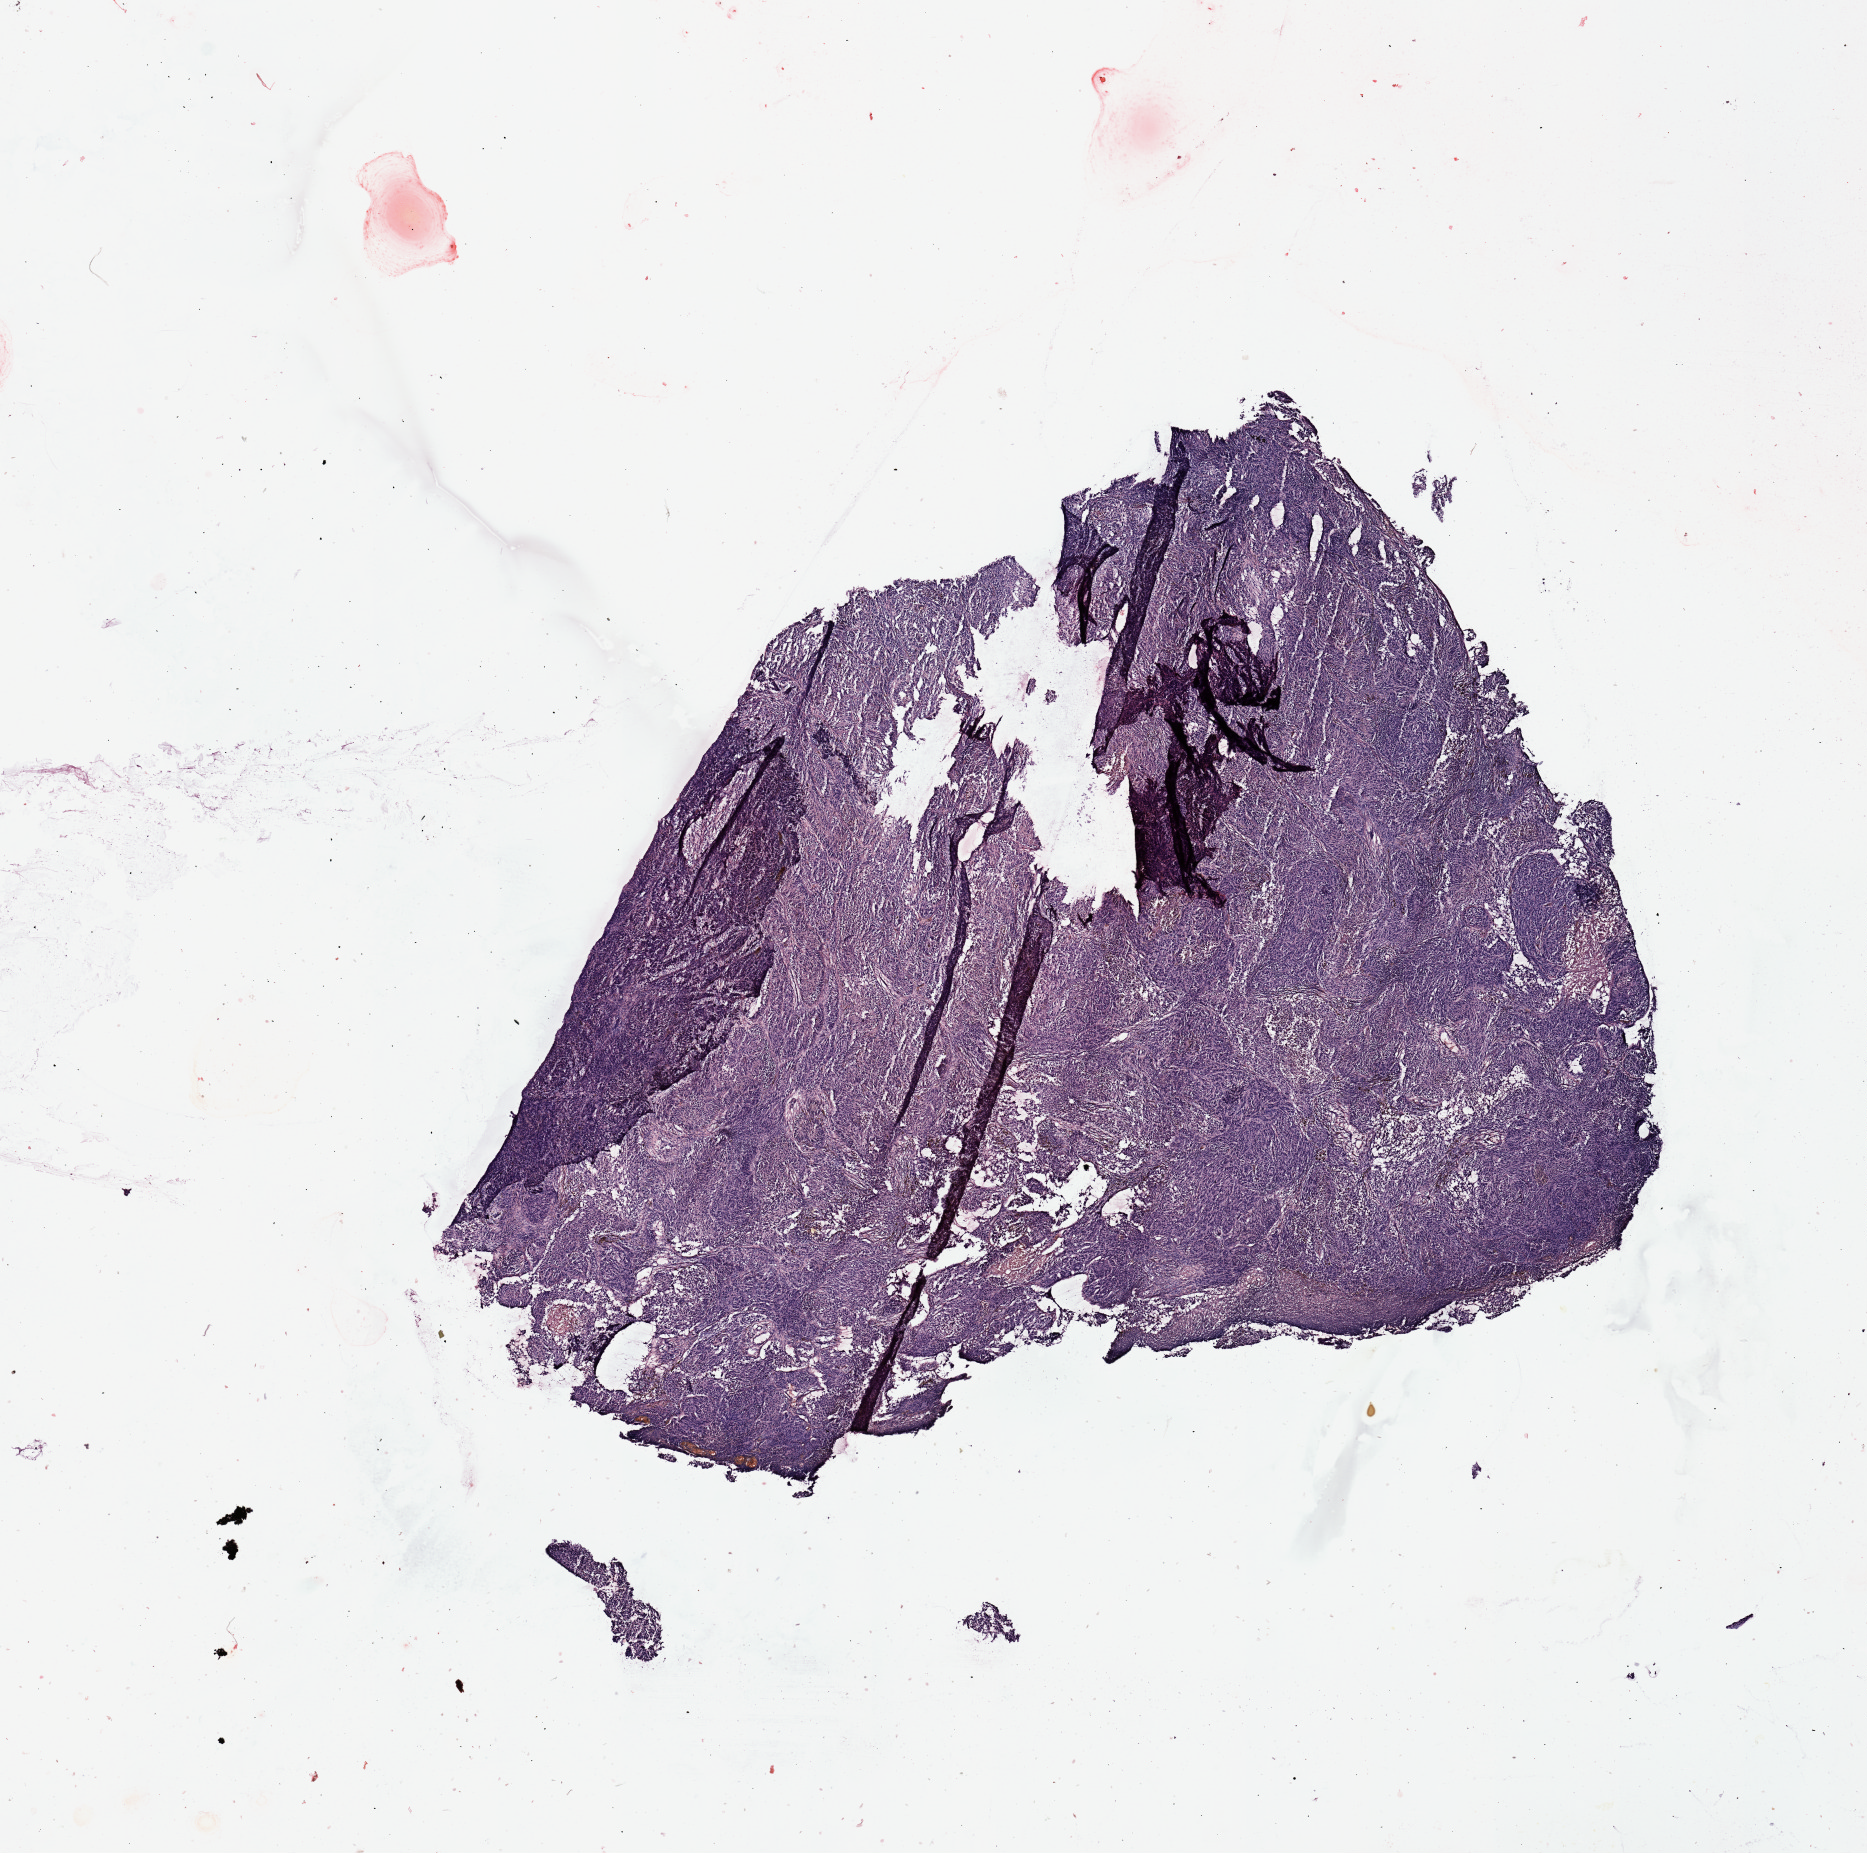
H&E whole-slide image — shown as a low-resolution overview of the whole scanned area (about 14.8 x 14.7 mm, slide scanned at 20x). Melanoma tumour tissue; sampled site not recorded. Male, 61 y/o.
Patient diagnosis (cohort enrolment): cutaneous melanoma (skin). Primary tumour site (as recorded): trunk.